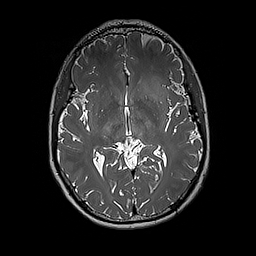
Brain MRI from a brain-tumour surgery series, one axial slice. Position 102 of 192 along the scan axis. 1 mm slice thickness. 256 × 256 image matrix, field of view 250 × 250 mm. From the clinical record (not read from this slice): histopathology: Glioblastoma; WHO grade: 4; IDH mutation: no; tumour location: Left Insular.
Outlined on this slice (expert manual segmentation):
- tumour: box from (x=140, y=76) to (x=171, y=113) px